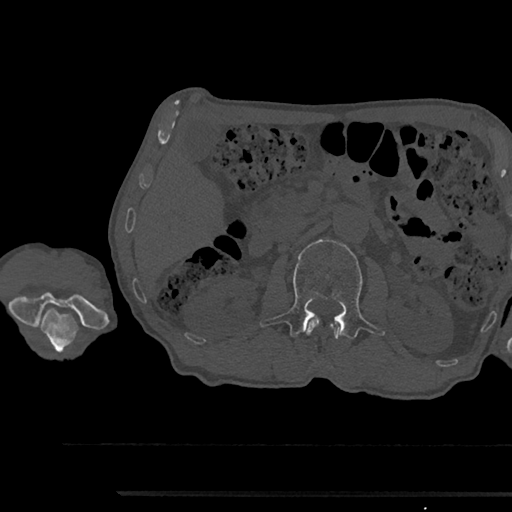
CT including the spine, one axial slice; slice 581 of 797 in the series (ordered by position); 120 kVp; bone window (W 1800 / L 400 HU); 0.5 mm slice thickness; 512 × 512 image matrix. Male patient, age 79 years. From the clinical record (not read from this slice): primary cancer: prostate.
Annotated regions visible in this slice (semi-automatically segmented with operator editing):
- L1 vertebra: bounding box (x1, y1, x2, y2) in pixels: (307, 318, 342, 340)
- L2 vertebra: (259, 239, 385, 339)